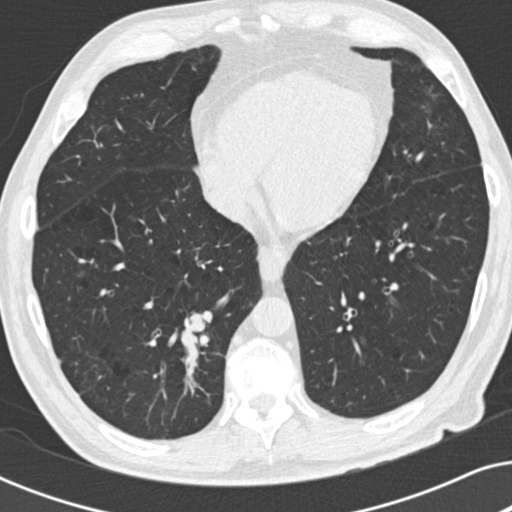
Low-dose screening chest CT, one axial slice; position 80 of 191 along the scan axis; reconstruction kernel B30f; 120 kVp; lung window (W 1500 / L -600 HU); 2 mm slice thickness; 512 × 512 image matrix, field of view 330 × 330 mm.
Structures marked on this image (manually delineated by an expert):
- lesion 1 (tumor, lower lobe of right lung): bounding box (x1, y1, x2, y2) in pixels: (180, 312, 209, 348)